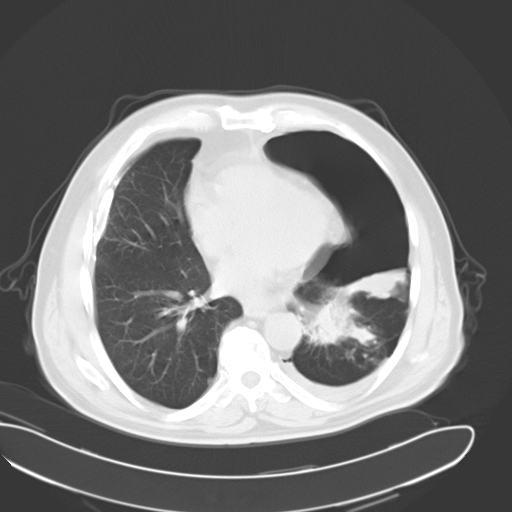
Chest CT, one axial slice; slice 16 of 34 in the series (ordered by position); reconstruction kernel B40f; 120 kVp; lung window (W 1500 / L -600 HU); 10 mm slice thickness; 512 × 512 image matrix, field of view 418 × 418 mm. Male patient, age 62 years. From the clinical record (not read from this slice): clinical TNM (as recorded): T3 N0 M1.
Annotated regions visible in this slice (rectangle marked by the reading radiologist):
- lung tumour (recorded histology: adenocarcinoma): bounding box <308,294,351,348> (left, top, right, bottom; pixels)
- lung tumour (recorded histology: adenocarcinoma): <313,293,354,353>